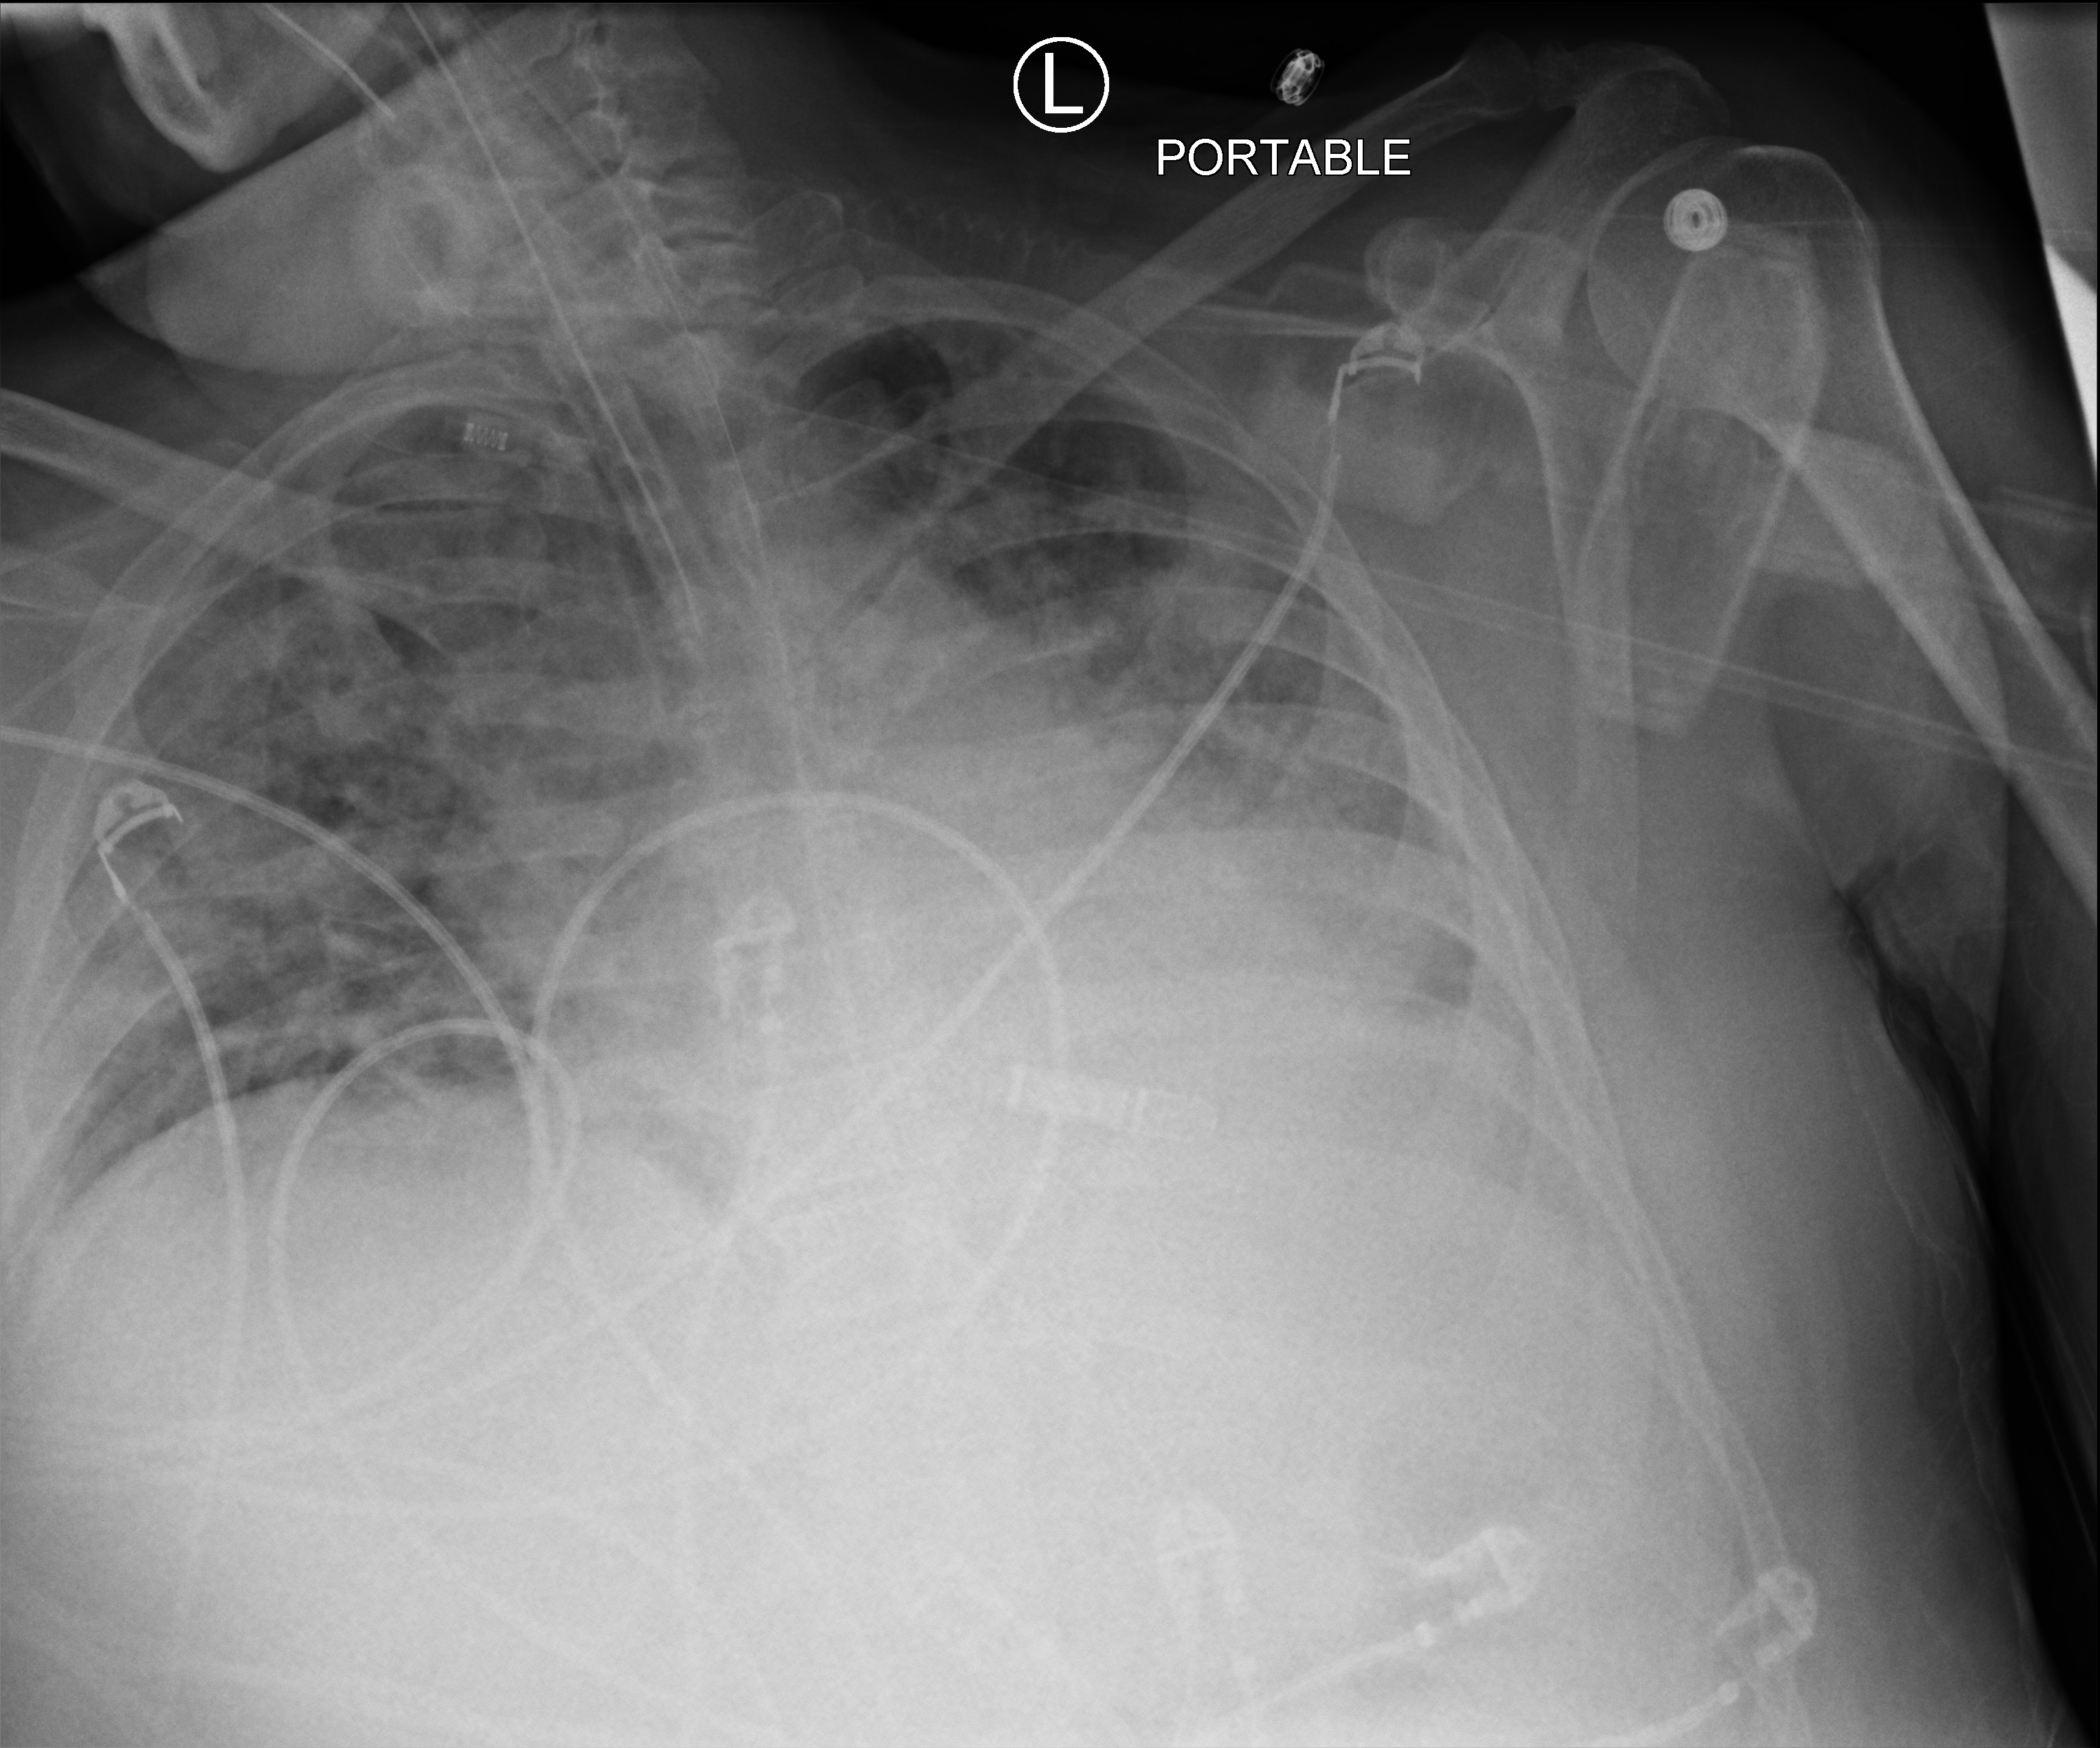
Bedside chest radiograph (computed radiography); anteroposterior (AP) projection. Patient hospitalised with COVID-19; male, aged 18–59 years.
Admission-level facts for this patient (not findings on this image; timing relative to this image not recorded):
- admitted to intensive care during this hospital stay: yes